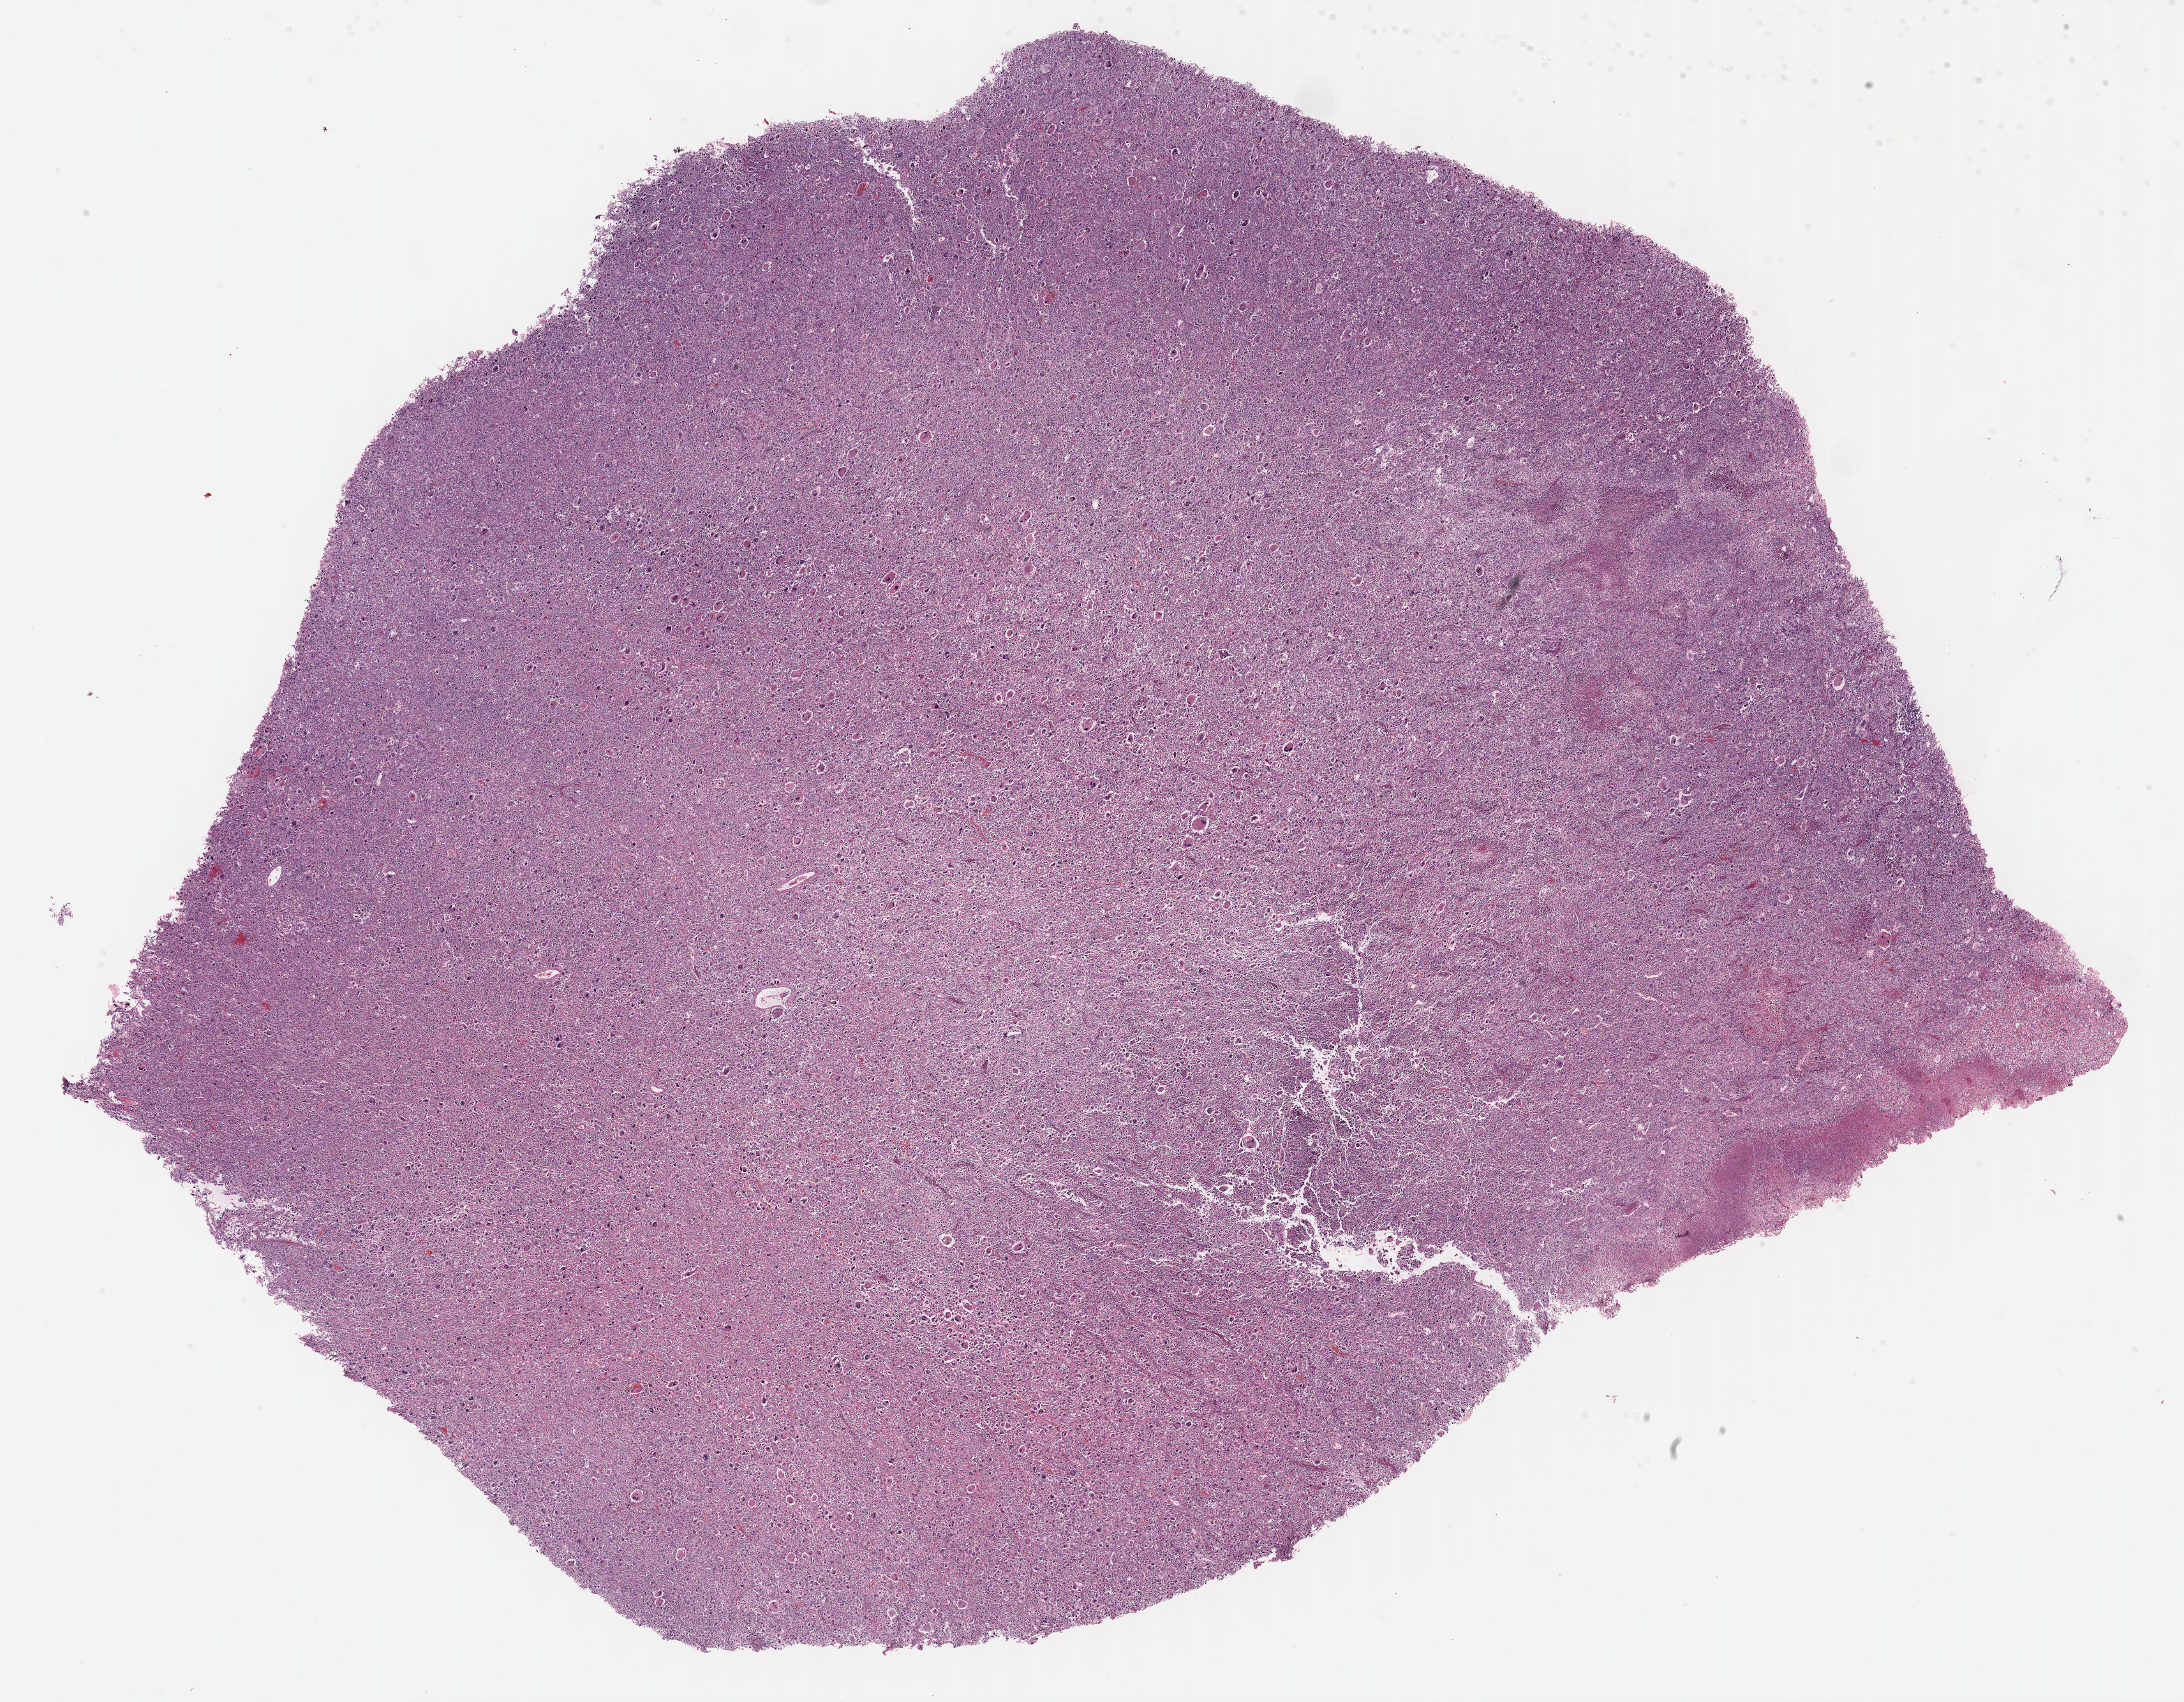
Hematoxylin and eosin (H&E) stained whole-slide image — shown as a low-resolution overview of the whole scanned area (about 27.7 x 21.6 mm, acquisition: 40x scan), FFPE section, primary tumour sample from the connective, subcutaneous and other soft tissues. Female patient; age at initial diagnosis 68 years.
Histologic diagnosis: Undifferentiated sarcoma.